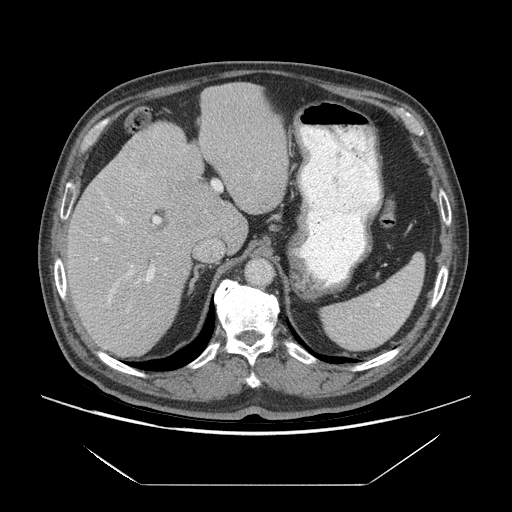
Contrast-enhanced abdominal CT (liver protocol), one axial slice. Slice 45 of 75 in the series (ordered by position). 140 kVp. Soft-tissue window (W 400 / L 40 HU). 512 × 512 image matrix, field of view 420 × 420 mm. From the clinical record (not read from this slice): diagnosis: hepatocellular carcinoma (patient treated with transarterial chemoembolisation; whether this scan precedes or follows treatment is not stated here); TNM stage (as recorded): Stage-I; Child-Pugh class: A; tumour differentiation: well differentiated; tumour nodularity: uninodular.
Outlined on this slice (semi-automatic segmentation, software-assisted and operator-edited):
- liver parenchyma outside the tumour (the mass and vessels are separate outlines, so this box may not span the whole liver): bounding box (x1, y1, x2, y2) in pixels: (66, 82, 288, 356)
- mass: (170, 182, 224, 231)
- liver vessels: (94, 155, 261, 312)